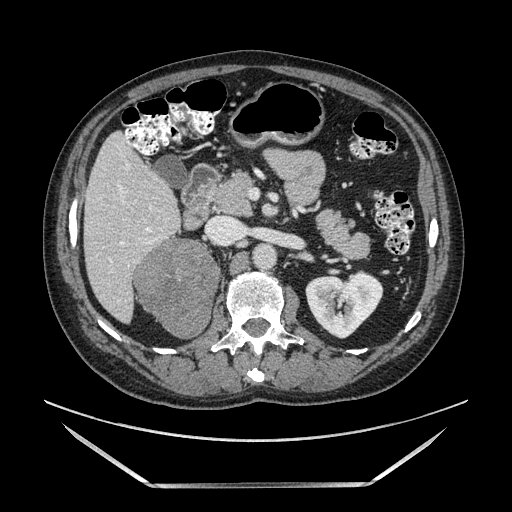
Contrast-enhanced abdominal CT, one axial slice; position 66 of 185 along the scan axis; soft-tissue window (W 400 / L 40 HU); 512 × 512 image matrix, field of view 440 × 440 mm. Male patient. Case-level facts recorded for this patient, not image findings: diagnosis: adrenocortical carcinoma; tumour side: right adrenal; tumour size at pathology: 10.3 cm; Ki-67 index: 20 %; stage (as recorded): 3.
Annotated regions visible in this slice (semi-automatic segmentation, software-assisted and operator-edited):
- mass: box from (x=136, y=240) to (x=219, y=338) px